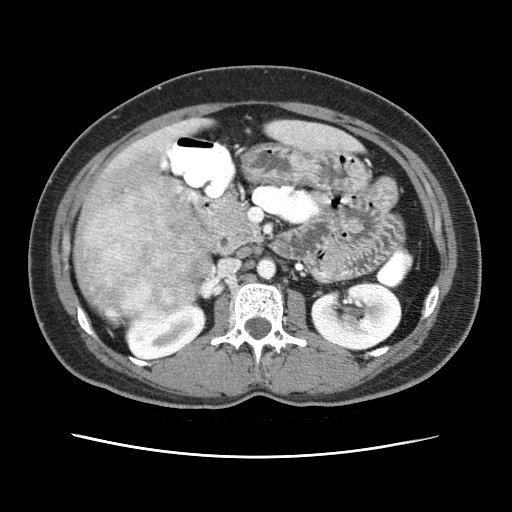
Contrast-enhanced abdominal CT (liver protocol), one axial slice. Slice 15 of 79 in the series (ordered by position). Reconstruction kernel STANDARD. 120 kVp. Soft-tissue window (W 400 / L 40 HU). 2.5 mm slice thickness. 512 × 512 image matrix, field of view 340 × 340 mm. From the clinical record (not read from this slice): diagnosis: hepatocellular carcinoma (patient treated with transarterial chemoembolisation; whether this scan precedes or follows treatment is not stated here); TNM stage (as recorded): Stage-I; Child-Pugh class: A; tumour differentiation: moderately differentiated; tumour nodularity: uninodular.
Outlined on this slice (semi-automatically segmented with operator editing):
- abdominal aorta: box from (x=257, y=257) to (x=276, y=277) px
- liver parenchyma outside the tumour (the mass and vessels are separate outlines, so this box may not span the whole liver): (x=74, y=118)–(x=298, y=320)
- mass: (x=75, y=153)–(x=209, y=321)
- liver vessels: (x=162, y=164)–(x=164, y=166)